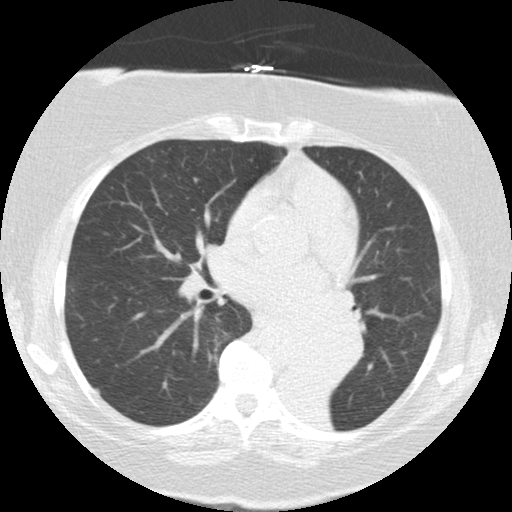
Chest CT (low-dose screening protocol), one axial image, baseline annual screen, lung window (W 1500 / L -600 HU), 2.5 mm slice thickness, standard (soft-tissue) reconstruction kernel (STANDARD), 120 kVp, slice 66 of 136 in the series. Female participant, aged 71 years at enrolment. Former smoker at enrolment.
Lesion marked by an expert reader, bounding box (x1, y1, x2, y2) in pixels: (285, 306, 365, 383). Reader record for this screening exam (exam-level; its link to the box is not recorded): non-calcified nodule or mass ≥4 mm, right middle lobe, 5 × 5 mm, smooth margins, soft tissue attenuation. Note: the box lies in the patient's left hemithorax on this image, whereas the reader's record names the right lung; they may be different findings. Participant outcome: lung cancer diagnosed 46 days after this screen — large cell carcinoma, NOS, left lower lobe, mediastinum, other location, poorly differentiated (G3), stage IV (AJCC 6th edition), 50 mm at pathology.